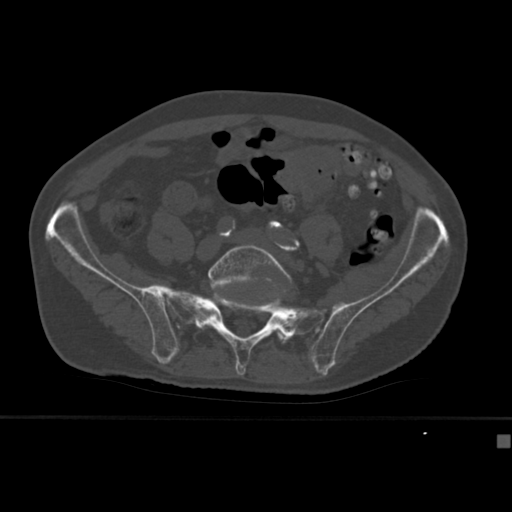
CT including the spine, one axial slice. Slice 77 of 430 in the series (ordered by position). Reconstruction kernel Br40s. 120 kVp. Bone window (W 1800 / L 400 HU). 1.5 mm slice thickness. 512 × 512 image matrix, field of view 337 × 337 mm. Male patient, age 64 years. From the clinical record (not read from this slice): primary cancer: uterus; vertebrae with lytic lesions (as recorded): T1, T4, T5, T7, L5.
Structures marked on this image (semi-automatically segmented with operator editing):
- L5 vertebra: bounding box (x1, y1, x2, y2) in pixels: (202, 244, 291, 344)